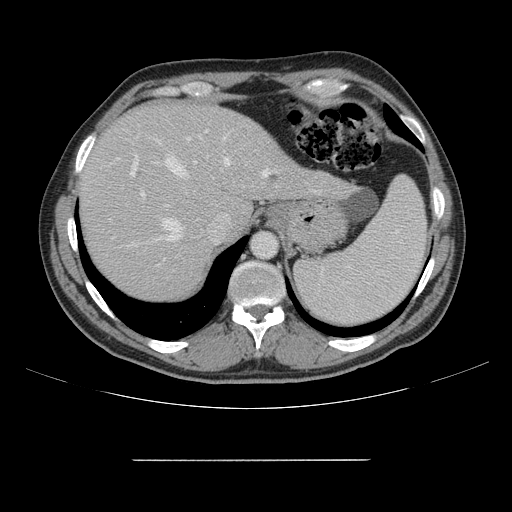
Contrast-enhanced abdominal CT, one axial slice; position 120 of 164 along the scan axis; soft-tissue window (W 400 / L 40 HU); 2.5 mm slice thickness; 512 × 512 image matrix, field of view 404 × 404 mm. Male patient, age 54 years. Case-level facts recorded for this patient, not image findings: diagnosis: colorectal cancer liver metastases, imaged before liver resection; multiple liver metastases: yes; largest metastasis: 1 cm.
Structures marked on this image (outlined manually by an expert reader):
- hepatic veins: box from (x=163, y=157) to (x=270, y=241) px
- liver: (x=80, y=104)–(x=347, y=299)
- planned liver remnant (the part of the liver to remain after resection): (x=80, y=104)–(x=252, y=299)
- portal vein (with intrahepatic branches): (x=117, y=137)–(x=277, y=272)
- liver metastasis: (x=271, y=176)–(x=277, y=180)